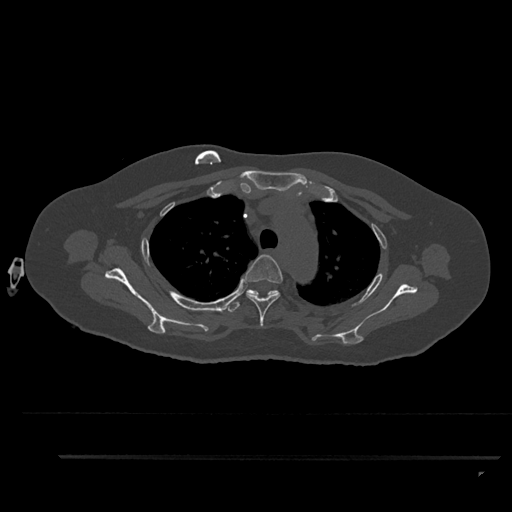
CT including the spine, one axial slice; slice 671 of 797 in the series (ordered by position); bone window (W 1800 / L 400 HU); 0.5 mm slice thickness; 512 × 512 image matrix, field of view 408 × 408 mm. Female patient, age 44 years. Case-level facts recorded for this patient, not image findings: primary cancer: renal; vertebrae with lytic lesions (as recorded): L1.
Annotated regions visible in this slice (semi-automatically segmented with operator editing):
- T3 vertebra: bounding box (x1, y1, x2, y2) in pixels: (242, 254, 283, 327)
- T4 vertebra: (227, 289, 279, 312)